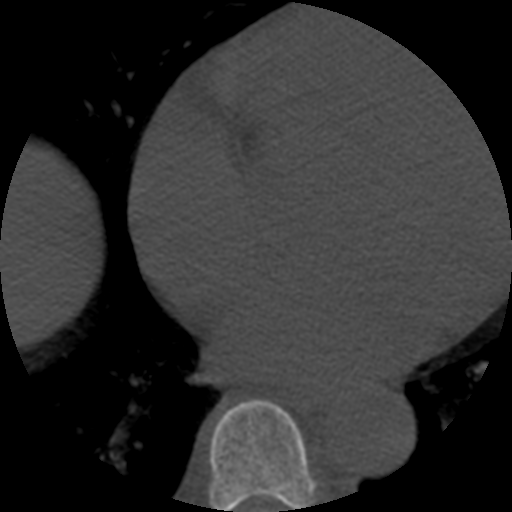
CT including the spine, one axial slice. Position 330 of 508 along the scan axis. Bone window (W 1800 / L 400 HU). 1.25 mm slice thickness. 512 × 512 image matrix, field of view 160 × 160 mm. Patient age 57 years. From the clinical record (not read from this slice): primary cancer: prostate.
Structures marked on this image (semi-automatically segmented with operator editing):
- T7 vertebra: bounding box <209,400,315,512> (left, top, right, bottom; pixels)